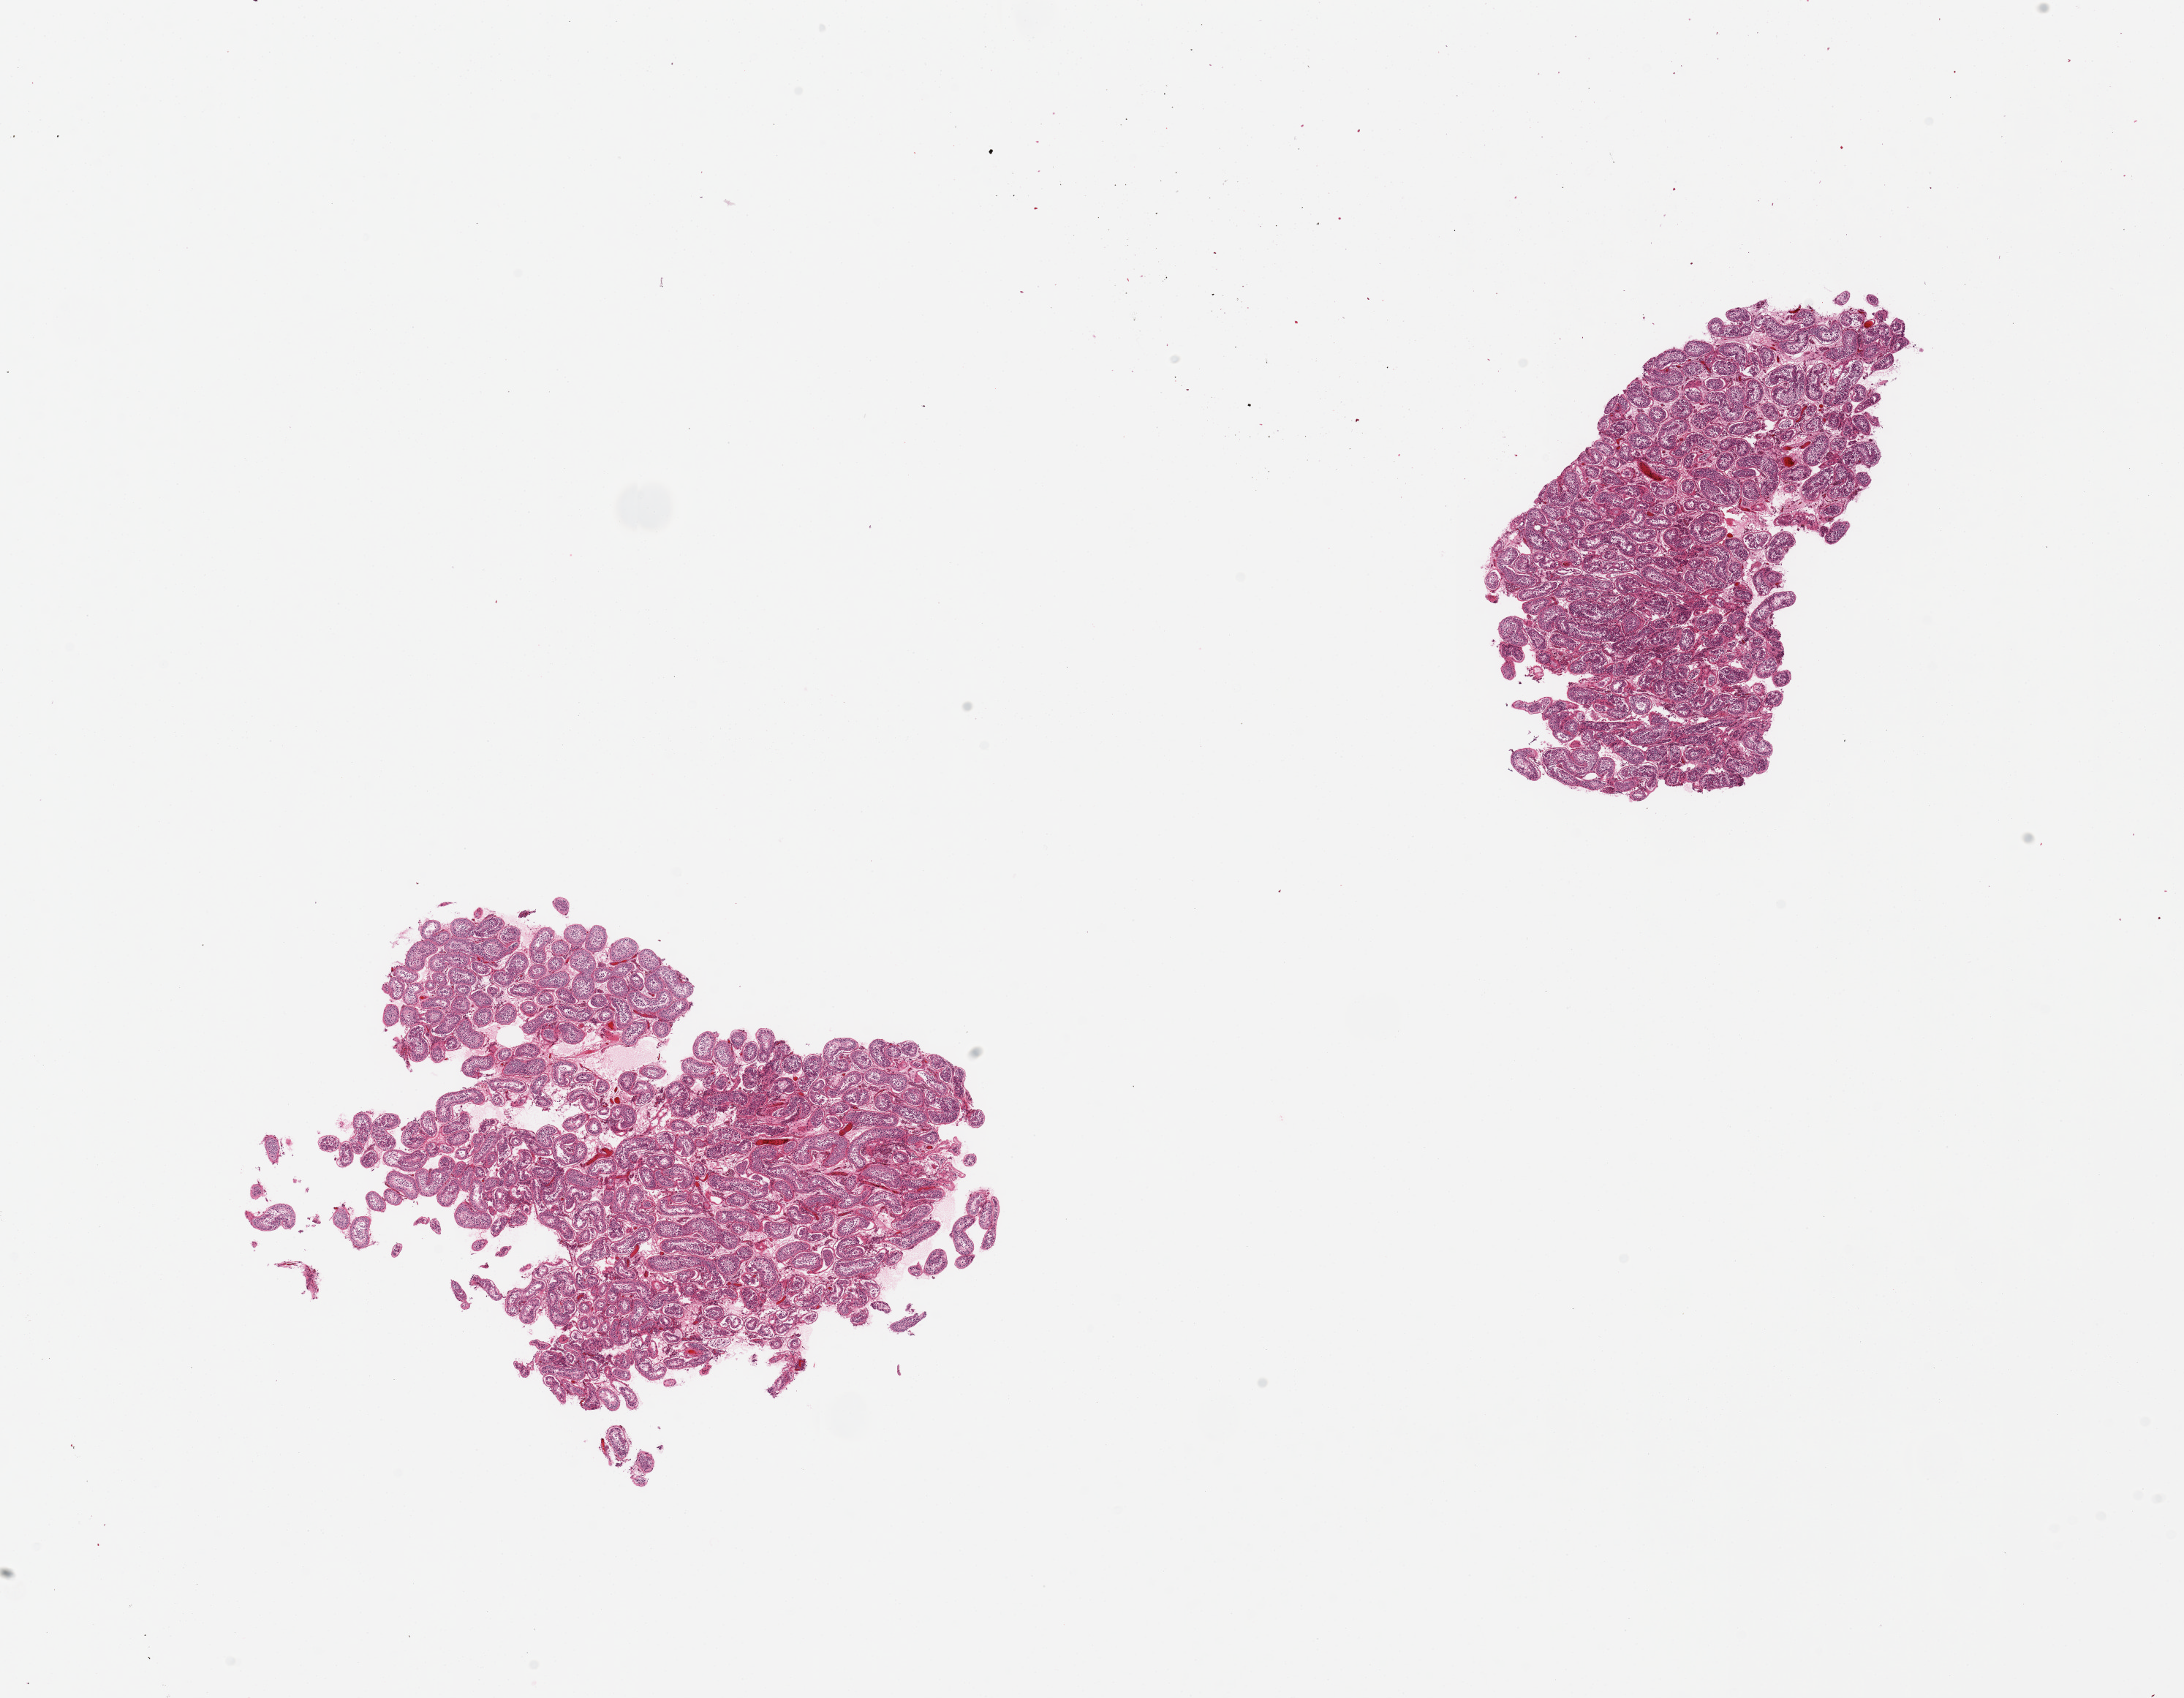
Digitized haematoxylin and eosin-stained section, low-resolution overview of the scanned area, about 23.6 x 18.4 mm. PAXgene-fixed paraffin-embedded (PFPE) section. Sampled site (target tissue): testis. Donor tissue sample. Donor: male.
Reviewer comment on this tissue sample: 2 pieces, fairly well preserved, spermatogenesis is present.